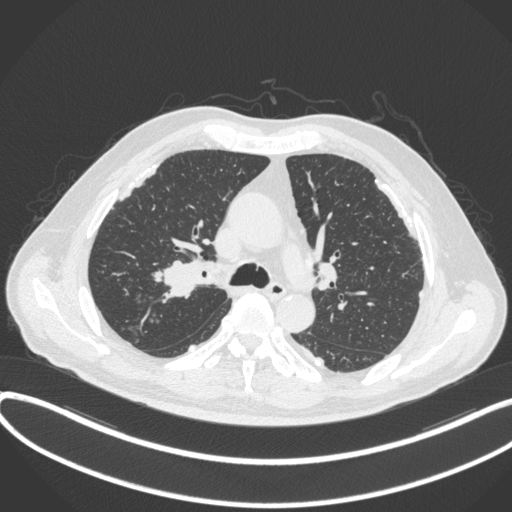
Chest CT, one axial slice. Reconstruction kernel B31f. 120 kVp. Lung window (W 1500 / L -600 HU). 1 mm slice thickness. 512 × 512 image matrix, field of view 400 × 400 mm. Patient: male, 58 years. Case-level facts recorded for this patient, not image findings: clinical TNM (as recorded): T1c N0 M0.
Structures marked on this image (bounding box drawn by a radiologist):
- lung tumour (recorded histology: squamous cell carcinoma): bounding box [x1, y1, x2, y2] px = [148, 257, 204, 304]